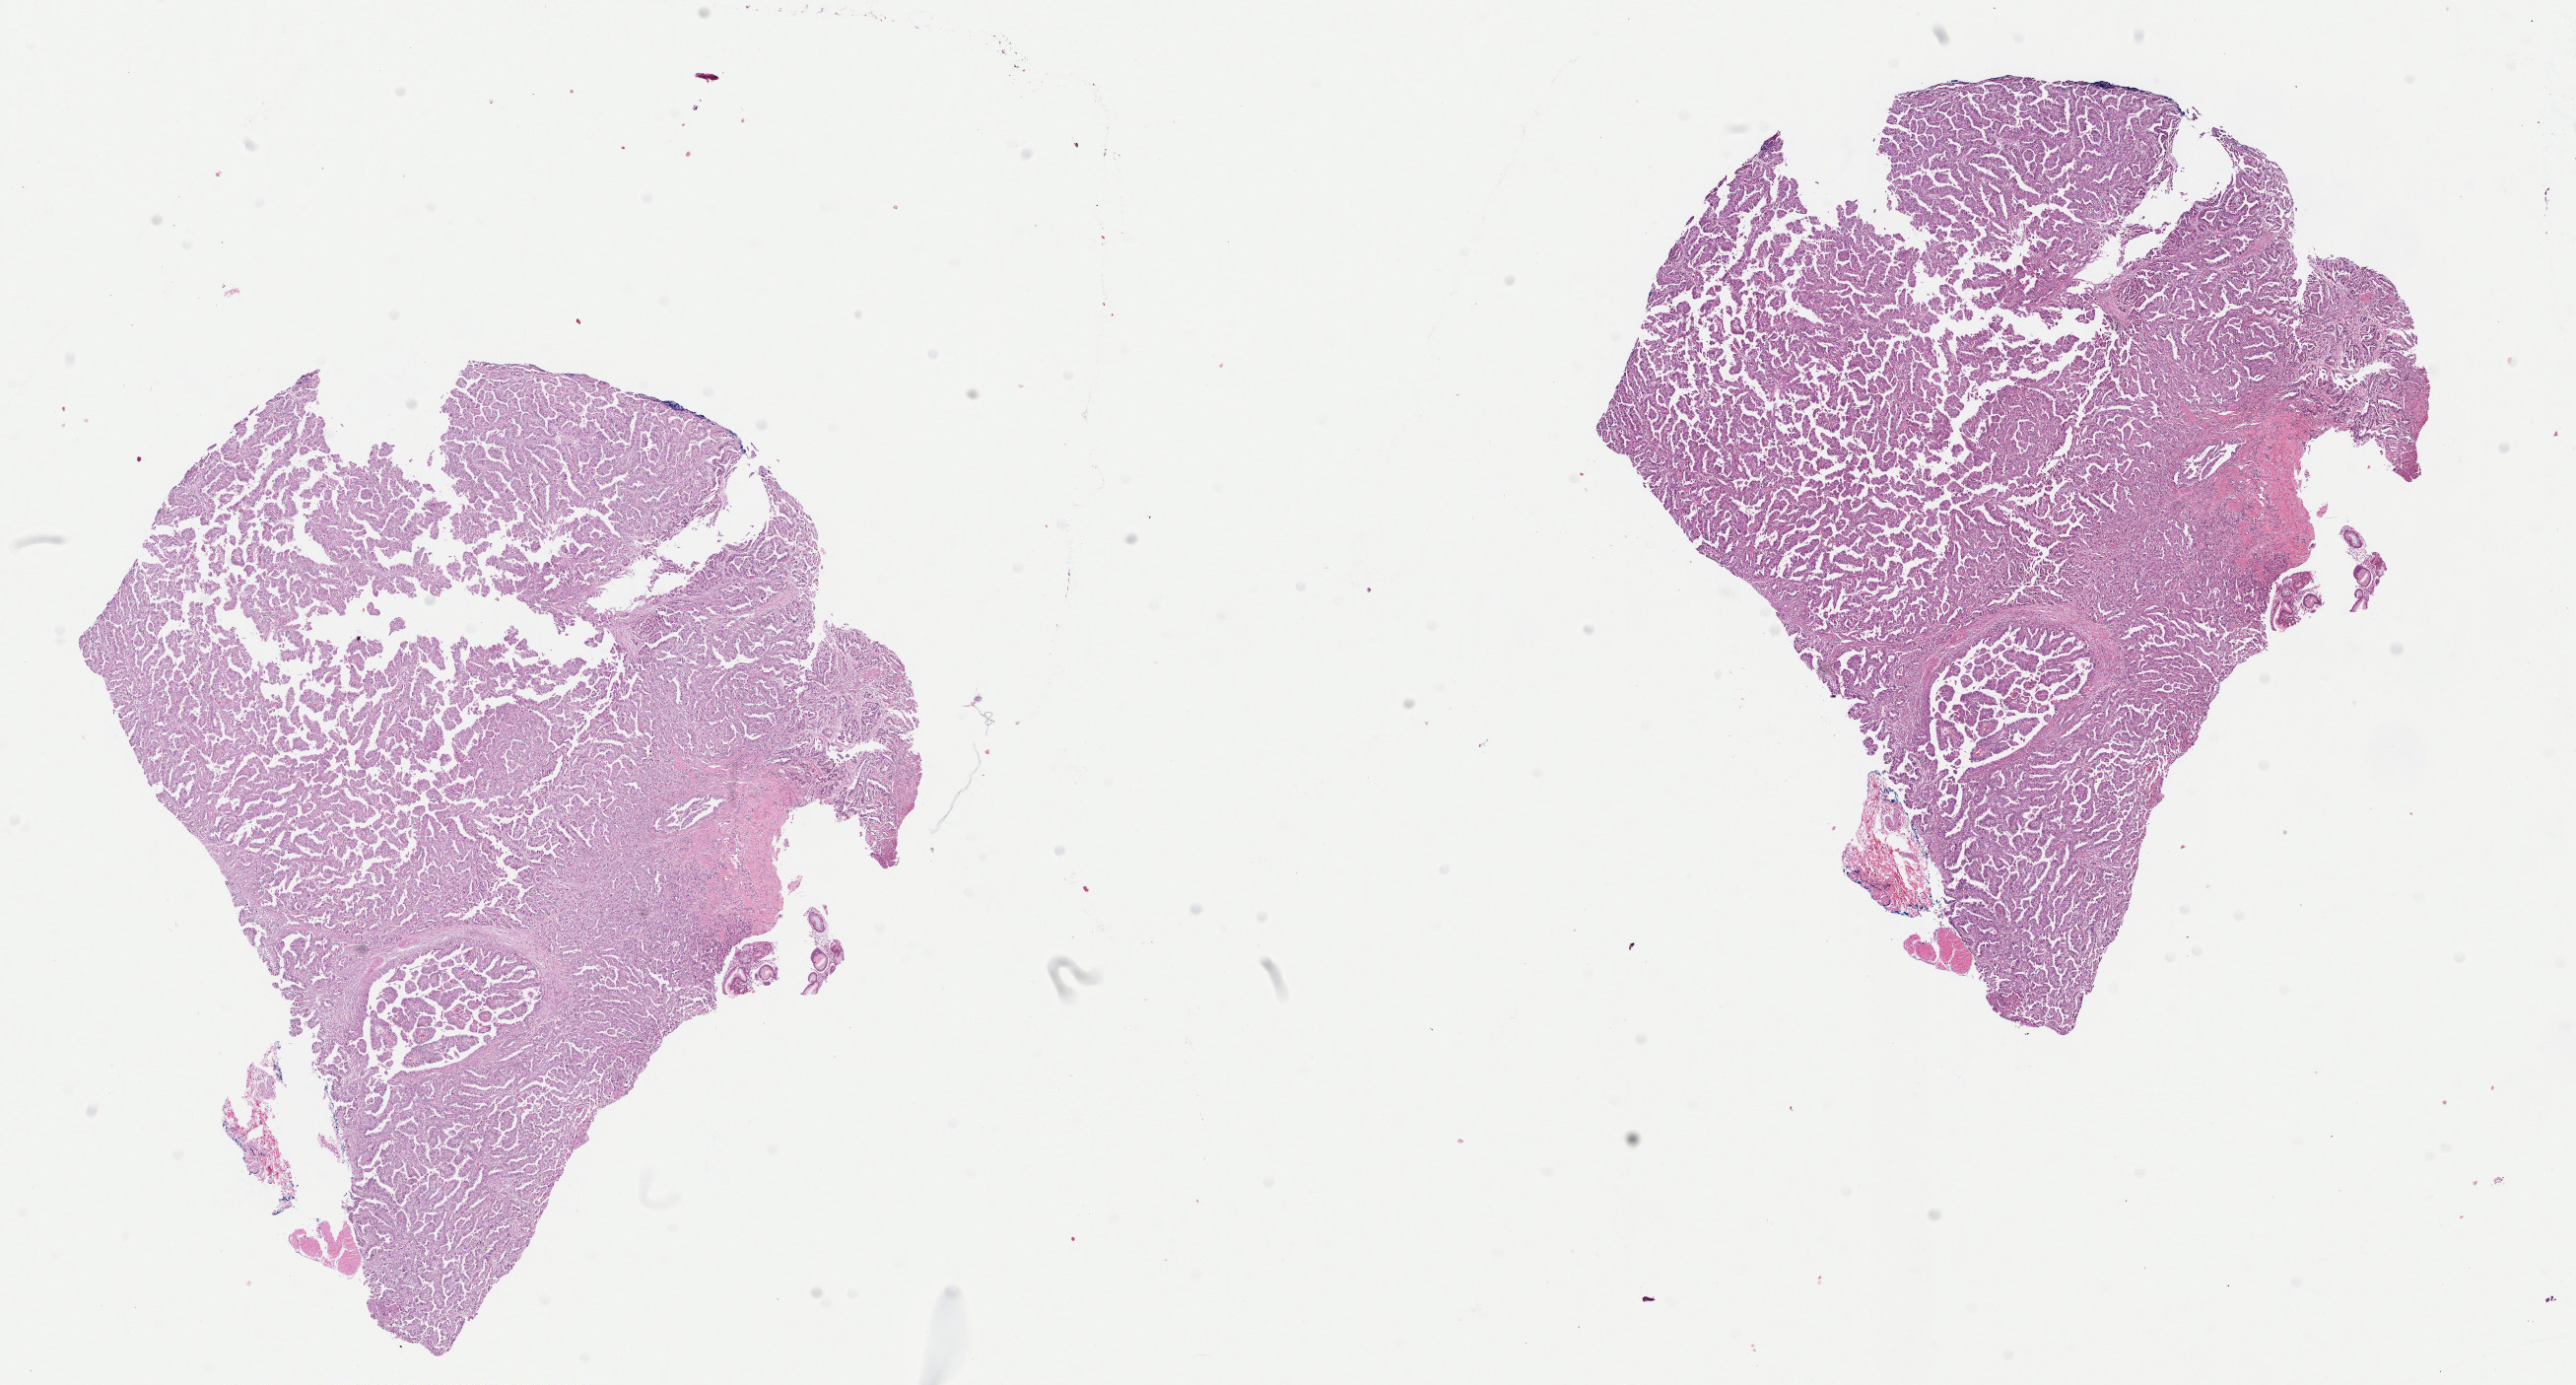
H&E-stained whole-slide image, shown as a low-resolution overview of the whole scanned area (about 20.7 x 11.1 mm); formalin-fixed paraffin-embedded (FFPE) diagnostic section; primary tumour sample from the stomach. Patient: male, age at initial diagnosis 73 years.
Diagnosis: Tubular adenocarcinoma.